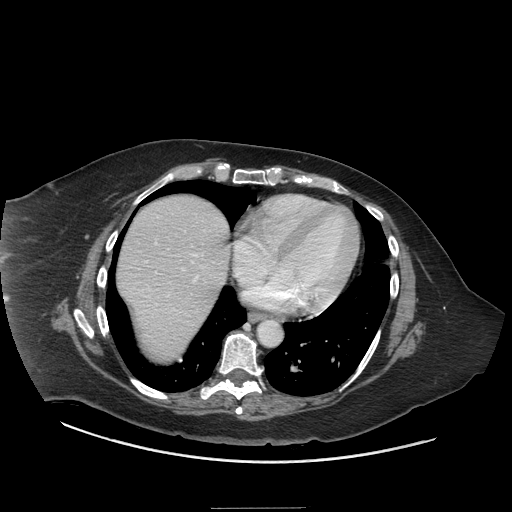
Contrast-enhanced abdominal CT (liver protocol), one axial slice. Position 67 of 81 along the scan axis. Soft-tissue window (W 400 / L 40 HU). 512 × 512 image matrix, field of view 440 × 440 mm. From the clinical record (not read from this slice): diagnosis: hepatocellular carcinoma (patient treated with transarterial chemoembolisation; whether this scan precedes or follows treatment is not stated here); TNM stage (as recorded): Stage-II; Child-Pugh class: A; tumour nodularity: multinodular; tumour size: 1.7 cm.
Outlined on this slice (semi-automatic segmentation, software-assisted and operator-edited):
- abdominal aorta: bounding box <258,320,281,346> (left, top, right, bottom; pixels)
- liver parenchyma outside the tumour (the mass and vessels are separate outlines, so this box may not span the whole liver): <116,196,230,359>
- liver vessels: <131,215,221,323>